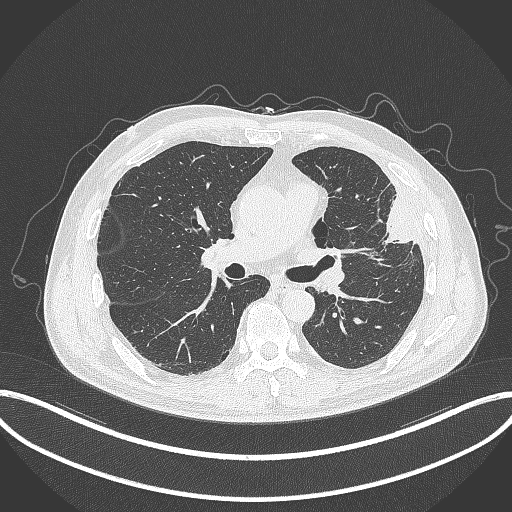
Chest CT, one axial slice; position 189 of 382 along the scan axis; reconstruction kernel B70f; lung window (W 1500 / L -600 HU); 512 × 512 image matrix, field of view 415 × 415 mm. Patient: male, 64 years. Case-level facts recorded for this patient, not image findings: clinical TNM (as recorded): T4 N1 M0; histopathological grade: G3.
Outlined on this slice (rectangle marked by the reading radiologist):
- lung tumour (recorded histology: adenocarcinoma): box from (x=371, y=191) to (x=422, y=247) px